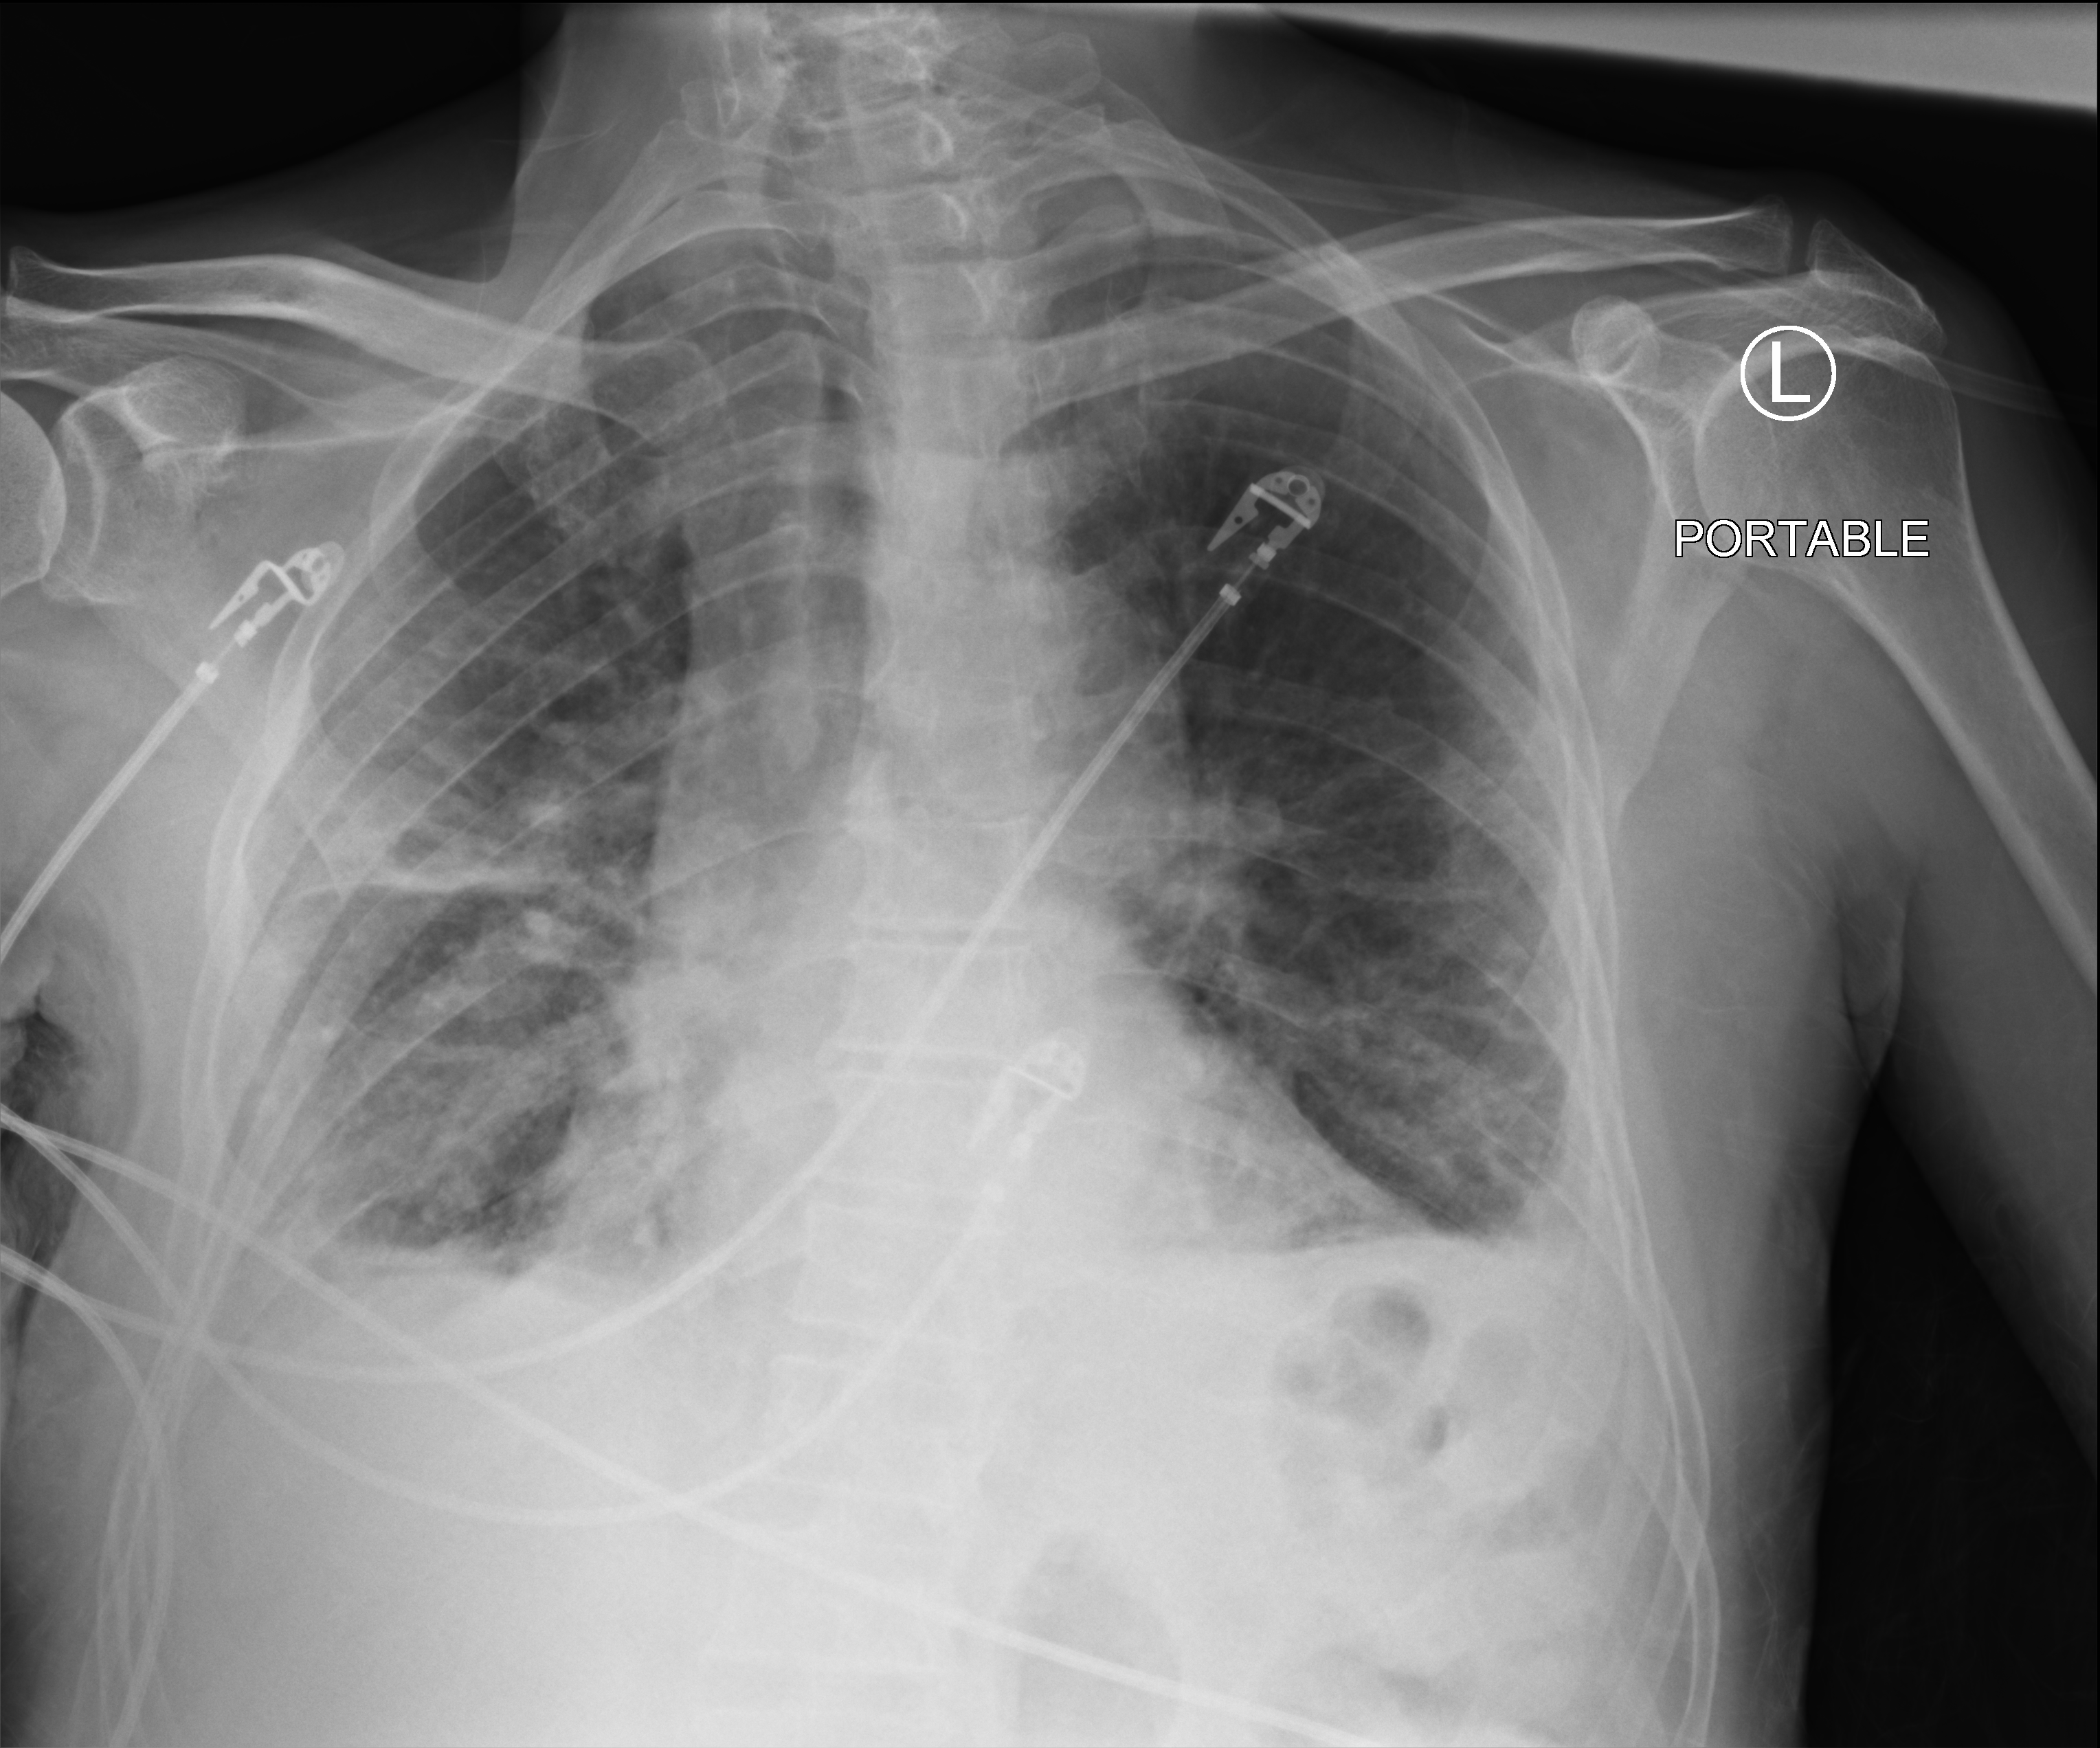
Chest X-ray (portable). Male patient hospitalised with COVID-19, age 75–90 years.
Admission-level facts for this patient (not findings on this image; timing relative to this image not recorded): admitted to intensive care during this hospital stay: yes.